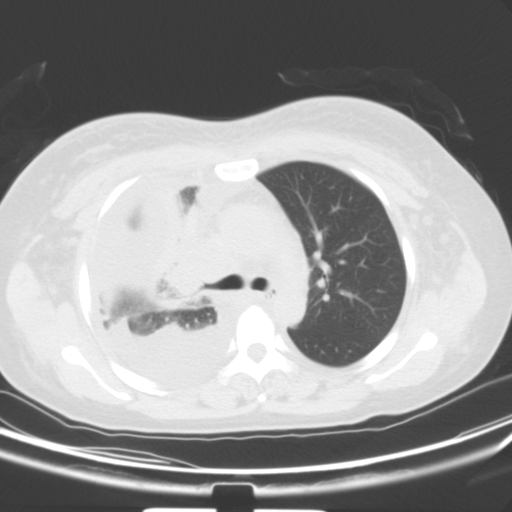
Chest CT, one axial slice; position 35 of 54 along the scan axis; 120 kVp; lung window (W 1500 / L -600 HU); 5 mm slice thickness; 512 × 512 image matrix, field of view 347 × 347 mm. Patient: female, 36 years. Case-level facts recorded for this patient, not image findings: clinical TNM (as recorded): T1b N2 M0; histopathological grade: G3.
Outlined on this slice (bounding box drawn by a radiologist):
- lung tumour (recorded histology: adenocarcinoma): bounding box [x1, y1, x2, y2] px = [178, 192, 228, 303]